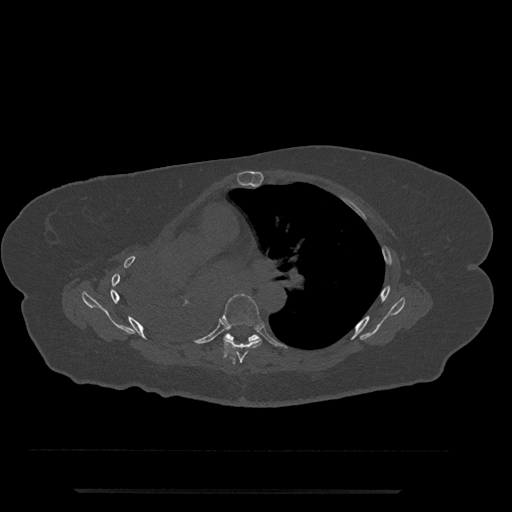
CT including the spine, one axial slice; slice 479 of 797 in the series (ordered by position); reconstruction kernel Br40s/3; 120 kVp; bone window (W 1800 / L 400 HU); 512 × 512 image matrix, field of view 440 × 440 mm. Female patient, age 51 years. From the clinical record (not read from this slice): primary cancer: neuro; vertebrae with lytic lesions (as recorded): T8.
Structures marked on this image (semi-automatic segmentation, software-assisted and operator-edited):
- T6 vertebra: bounding box <219,294,263,364> (left, top, right, bottom; pixels)
- T7 vertebra: <225,333,260,341>